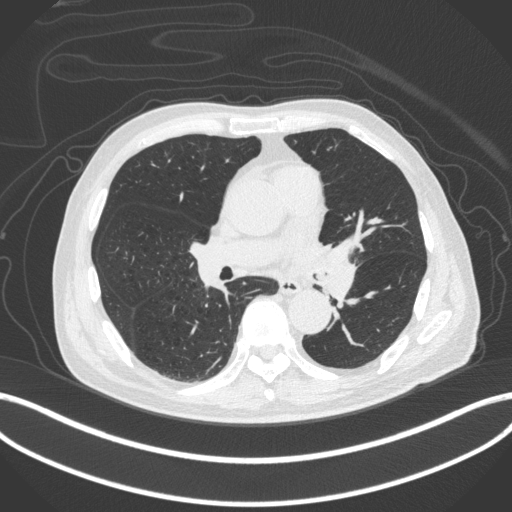
Chest CT, one axial slice. Slice 229 of 420 in the series (ordered by position). Lung window (W 1500 / L -600 HU). 1 mm slice thickness. 512 × 512 image matrix, field of view 400 × 400 mm. Male patient, age 77 years. From the clinical record (not read from this slice): clinical TNM (as recorded): T3 N1 M0.
Outlined on this slice (rectangle marked by the reading radiologist):
- lung tumour (recorded histology: adenocarcinoma): bounding box <316,240,364,306> (left, top, right, bottom; pixels)